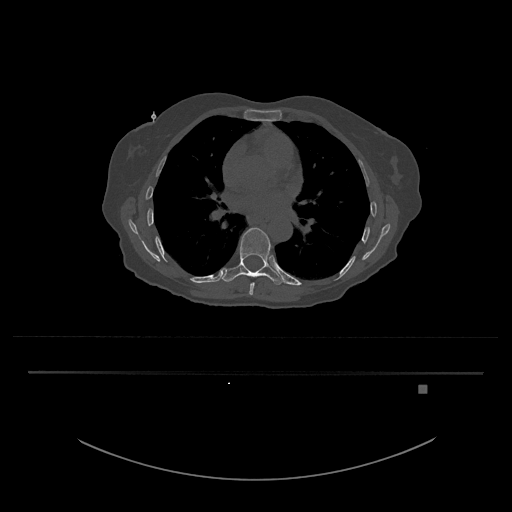
CT including the spine, one axial slice; slice 769 of 797 in the series (ordered by position); reconstruction kernel Br40s/3; 120 kVp; bone window (W 1800 / L 400 HU); 0.5 mm slice thickness; 512 × 512 image matrix. Patient: female, 57 years. From the clinical record (not read from this slice): primary cancer: cervical.
Outlined on this slice (semi-automatic segmentation, software-assisted and operator-edited):
- T8 vertebra: bounding box <249,282,255,295> (left, top, right, bottom; pixels)
- T9 vertebra: <222,227,285,285>